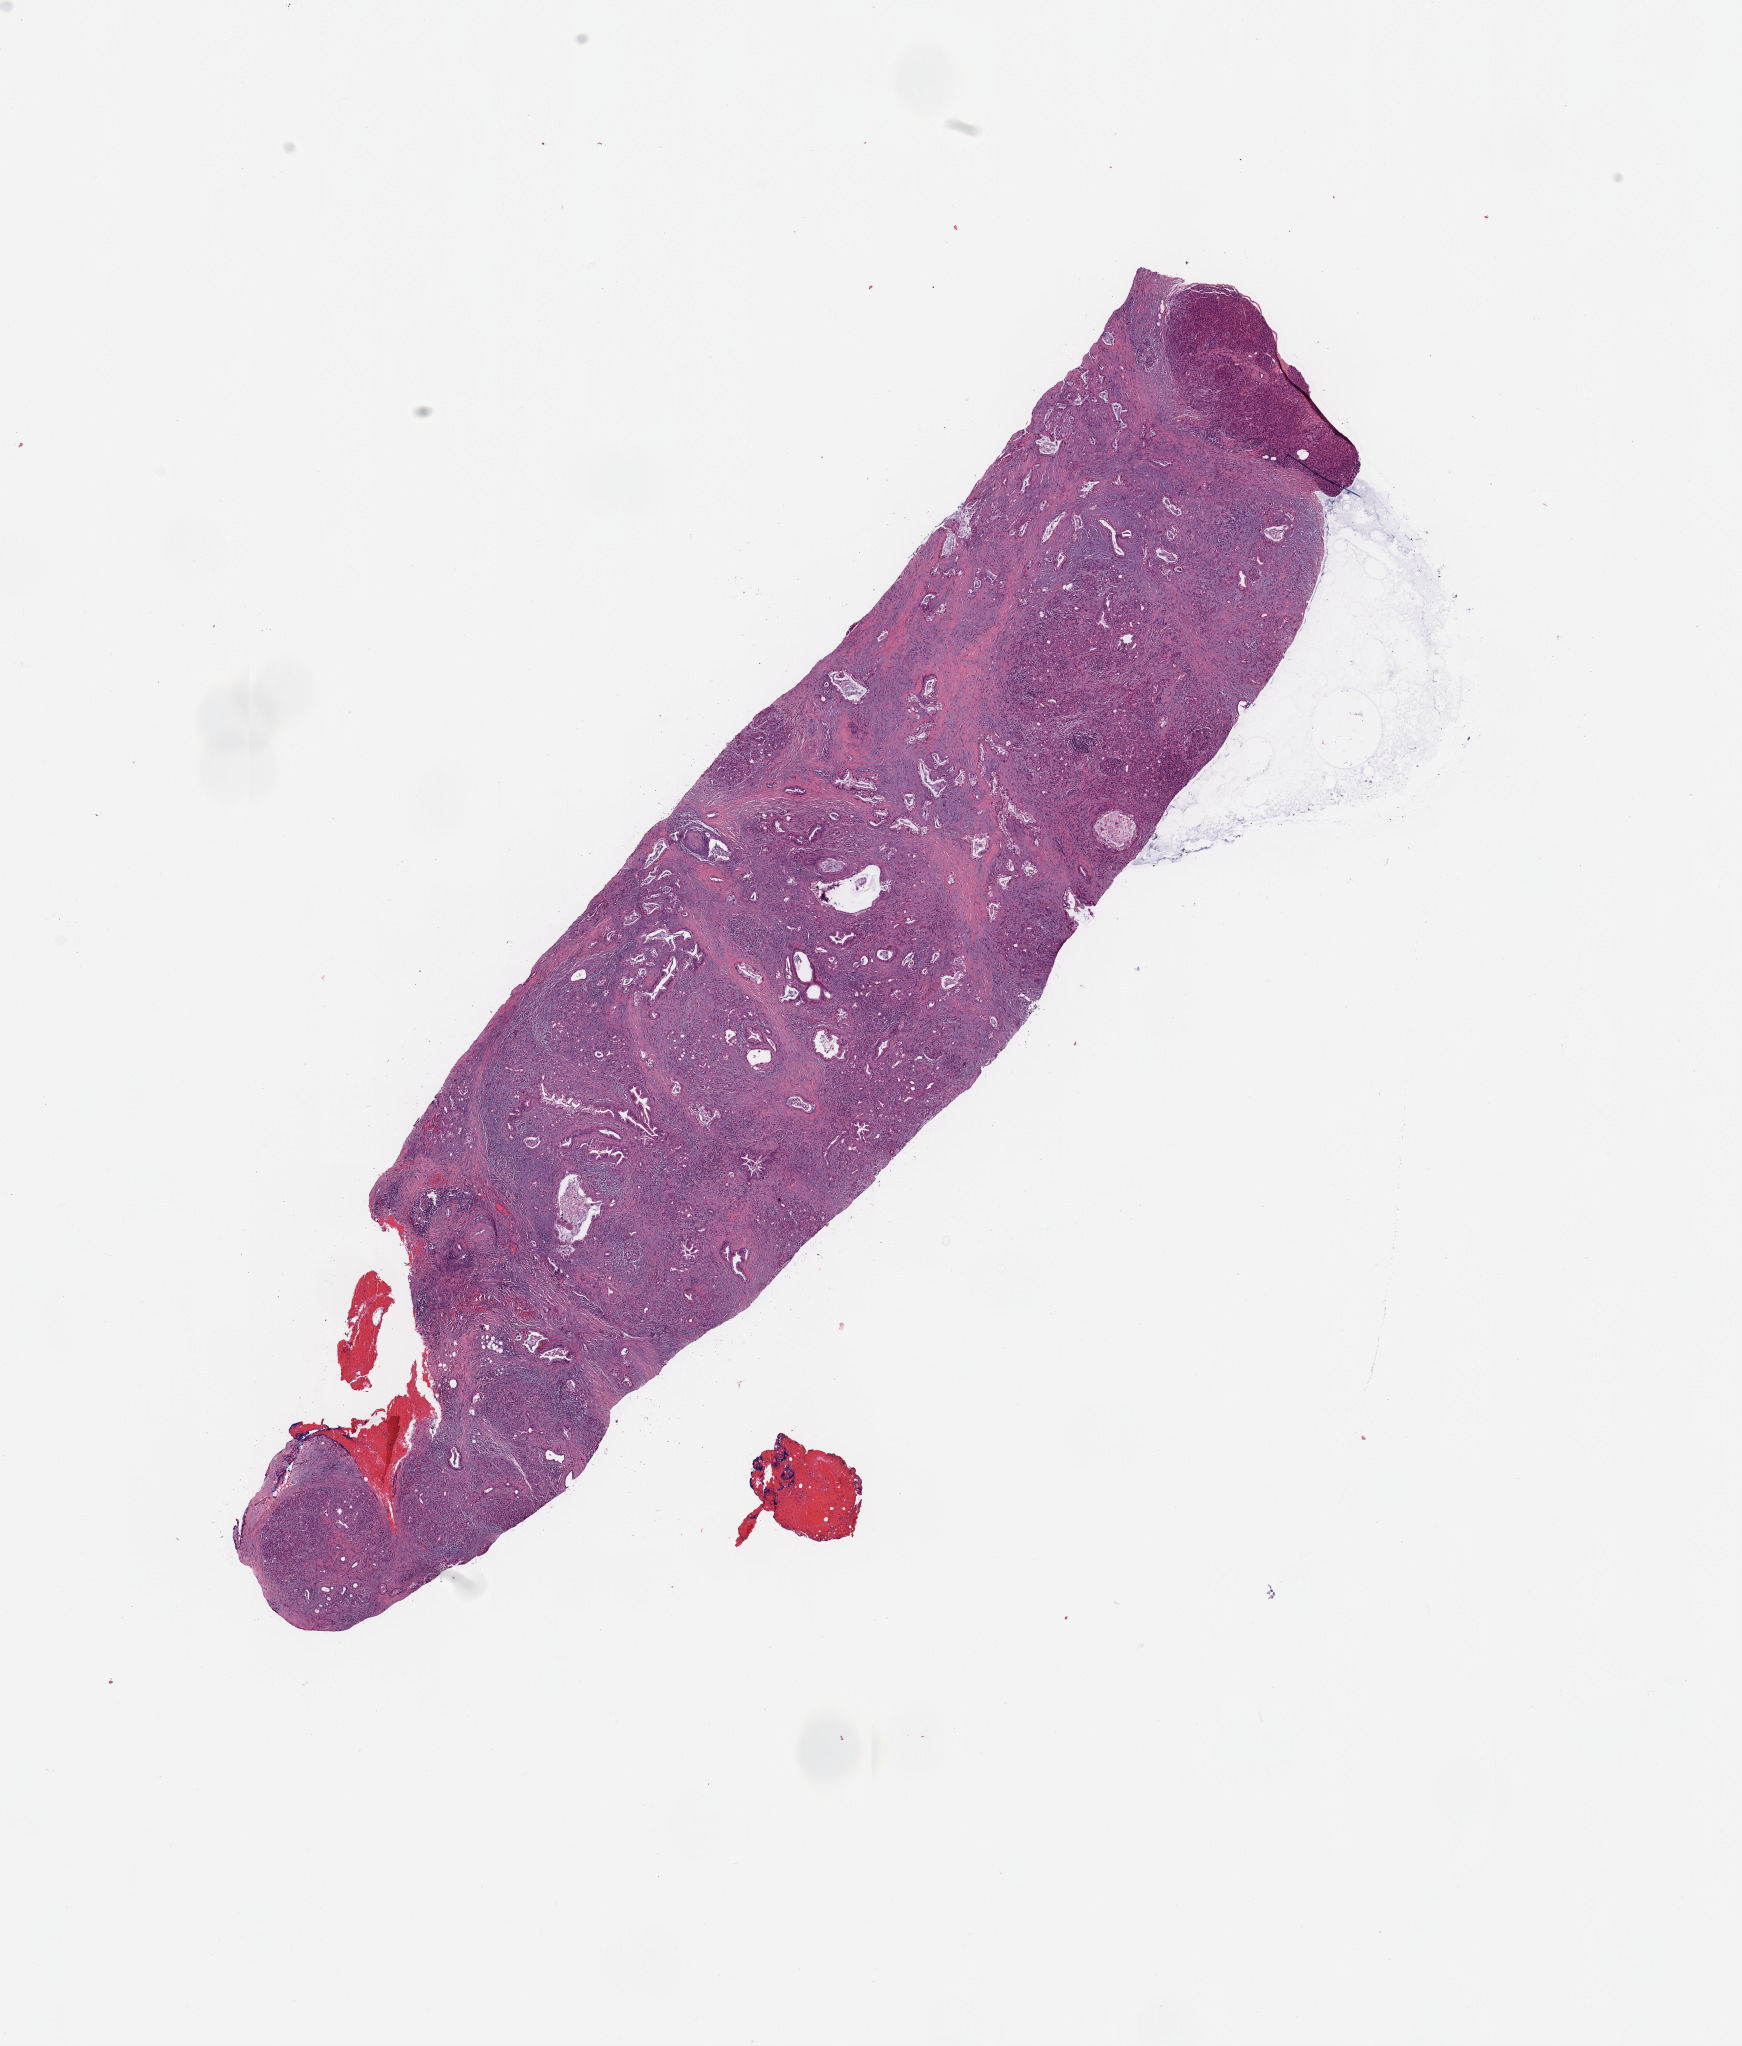
H&E whole-slide image, a low-resolution overview of the entire scanned area, about 13.8 x 16.2 mm (acquisition: 20x scan); tumour tissue sample, sampled site: pancreas. 80-year-old male patient. Histologic grade: G2 (moderately differentiated). Pathologist review of this section (percent, as recorded): tumour nuclei 25%, necrosis 0%.
- AJCC pathologic stage: IIB
- diagnosis: Infiltrating duct carcinoma, NOS
- primary tumour site (as recorded): head